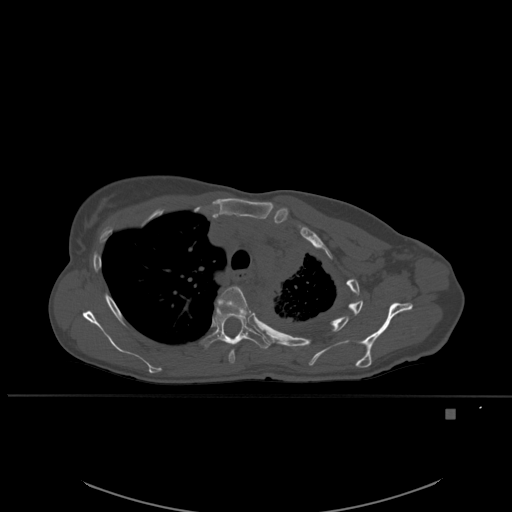
CT including the spine, one axial slice. Position 404 of 537 along the scan axis. Bone window (W 1800 / L 400 HU). 1.5 mm slice thickness. 512 × 512 image matrix, field of view 440 × 440 mm. Female patient, age 45 years. From the clinical record (not read from this slice): primary cancer: lung.
Structures marked on this image (semi-automatically segmented with operator editing):
- T4 vertebra: box from (x=216, y=286) to (x=251, y=364) px
- T5 vertebra: (x=202, y=306)–(x=271, y=349)